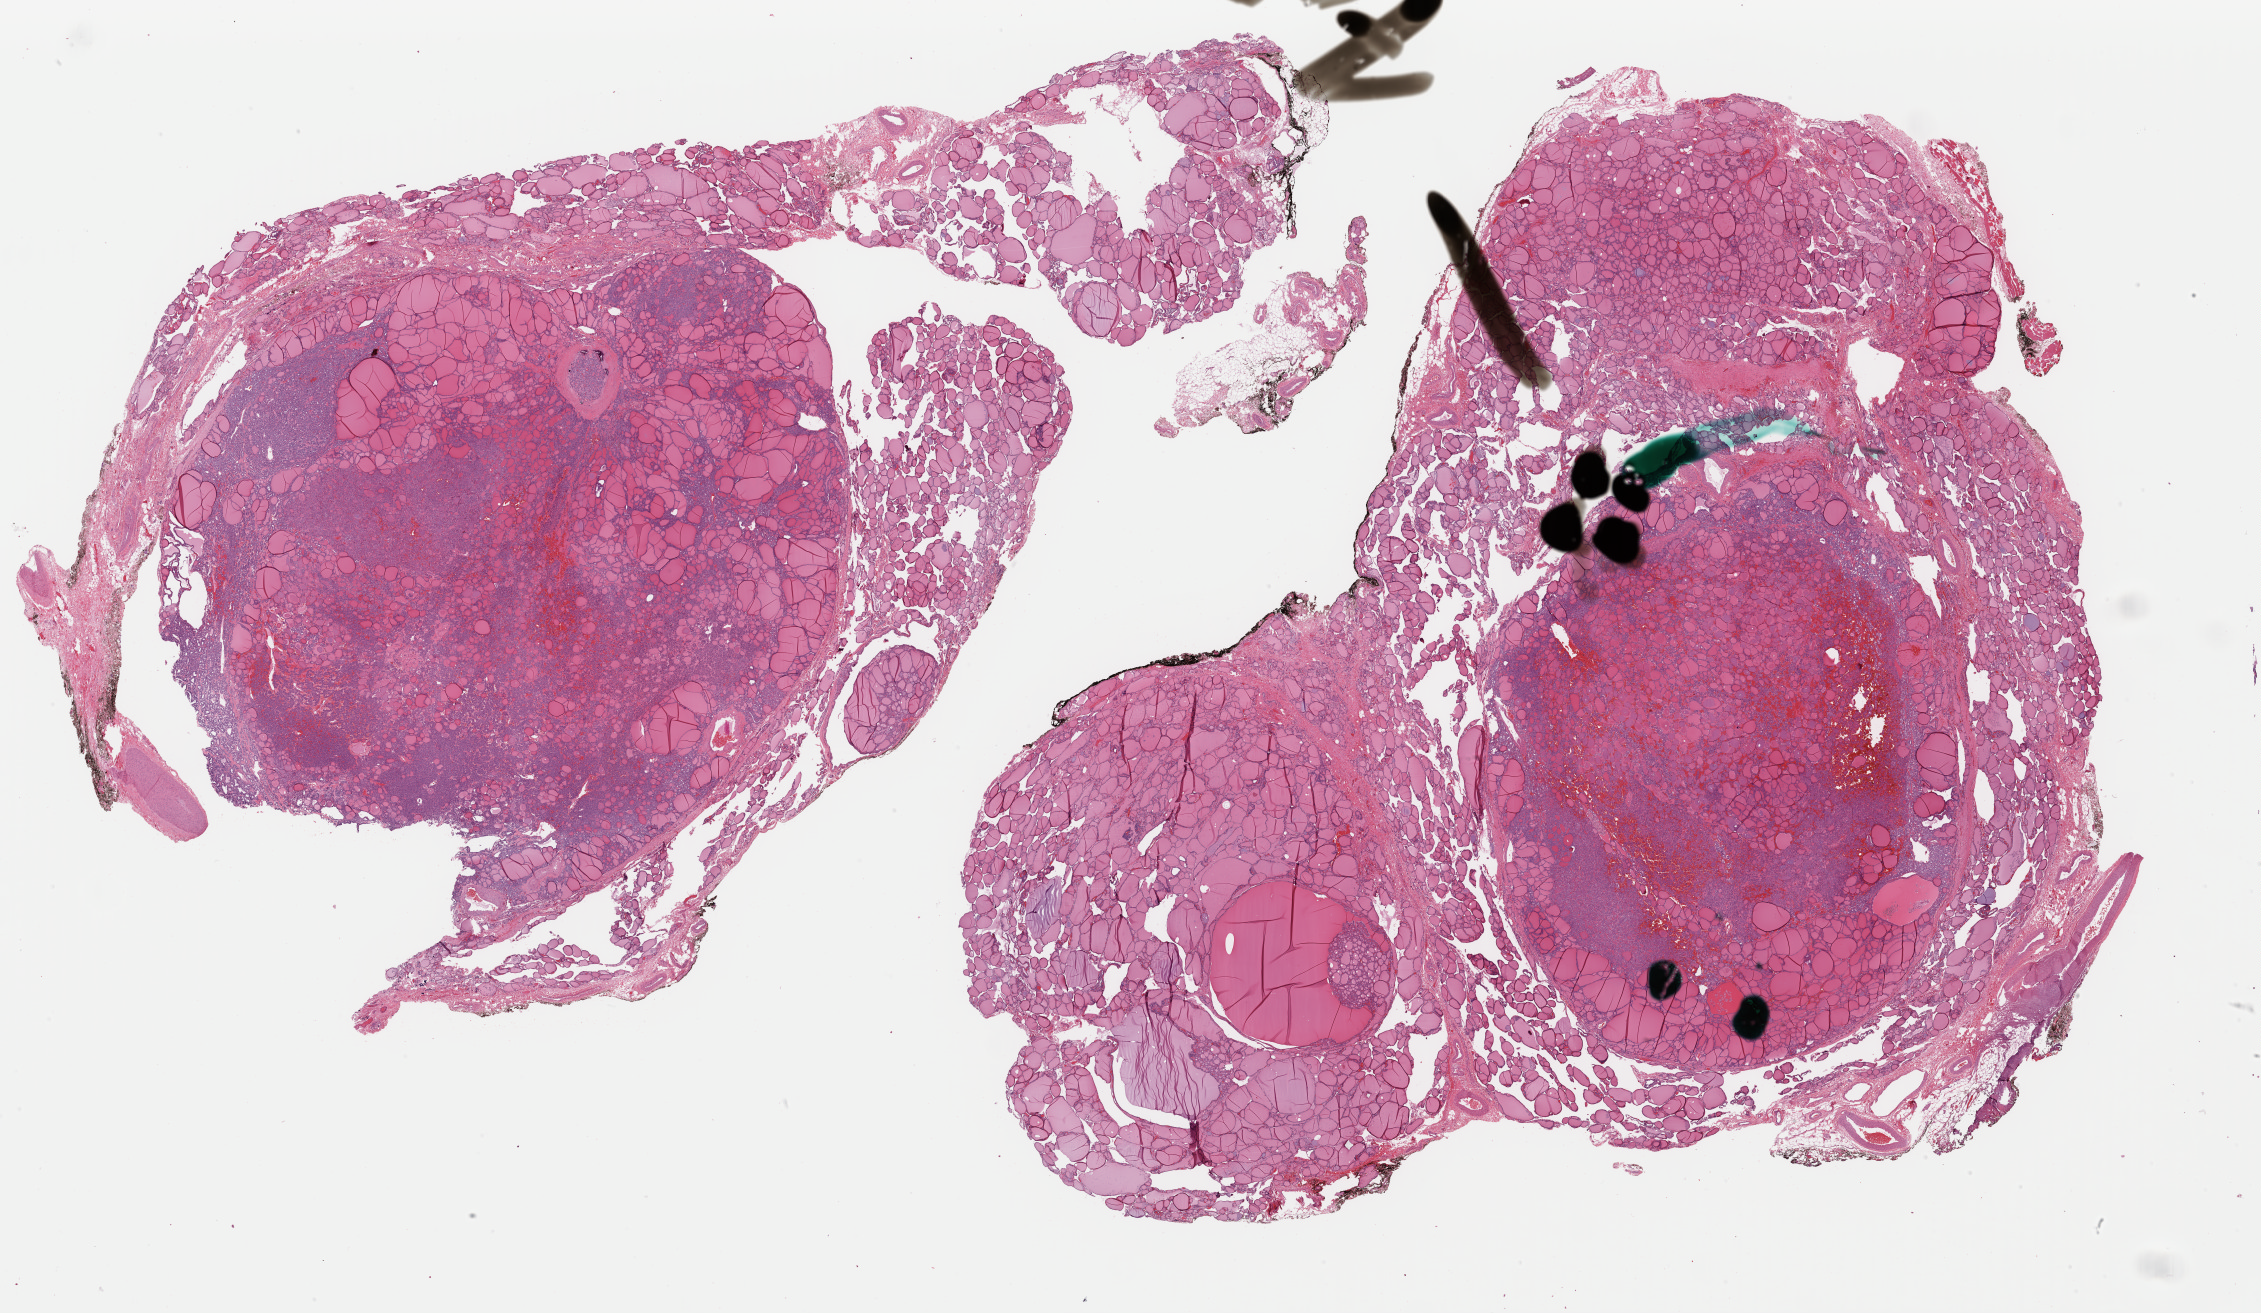
H&E whole-slide image — shown as a low-resolution overview of the whole scanned area (about 35.7 x 20.7 mm). Formalin-fixed paraffin-embedded (FFPE) diagnostic section. Thyroid, primary tumour sample. Female, age 48 years at initial diagnosis.
TNM: T2 N1 M0. Lymph nodes positive (case pathology): 4 of 7 examined. Pathologic diagnosis: Papillary carcinoma, follicular variant (thyroid gland). AJCC pathologic stage: III.